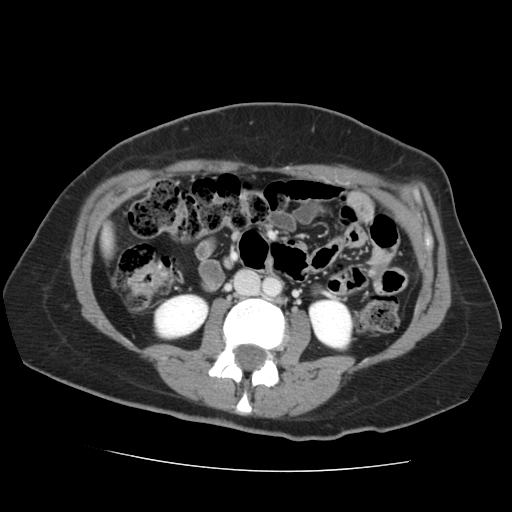
Contrast-enhanced abdominal CT, one axial slice; slice 39 of 144 in the series (ordered by position); intravenous contrast given; soft-tissue window (W 400 / L 40 HU); 2.5 mm slice thickness; 512 × 512 image matrix, field of view 333 × 333 mm. Female patient, age 46 years. Case-level facts recorded for this patient, not image findings: diagnosis: colorectal cancer liver metastases, imaged before liver resection; multiple liver metastases: no; largest metastasis: 2.8 cm; disease in both lobes: no.
Annotated regions visible in this slice (outlined manually by an expert reader):
- liver: bounding box (x1, y1, x2, y2) in pixels: (104, 234, 111, 250)